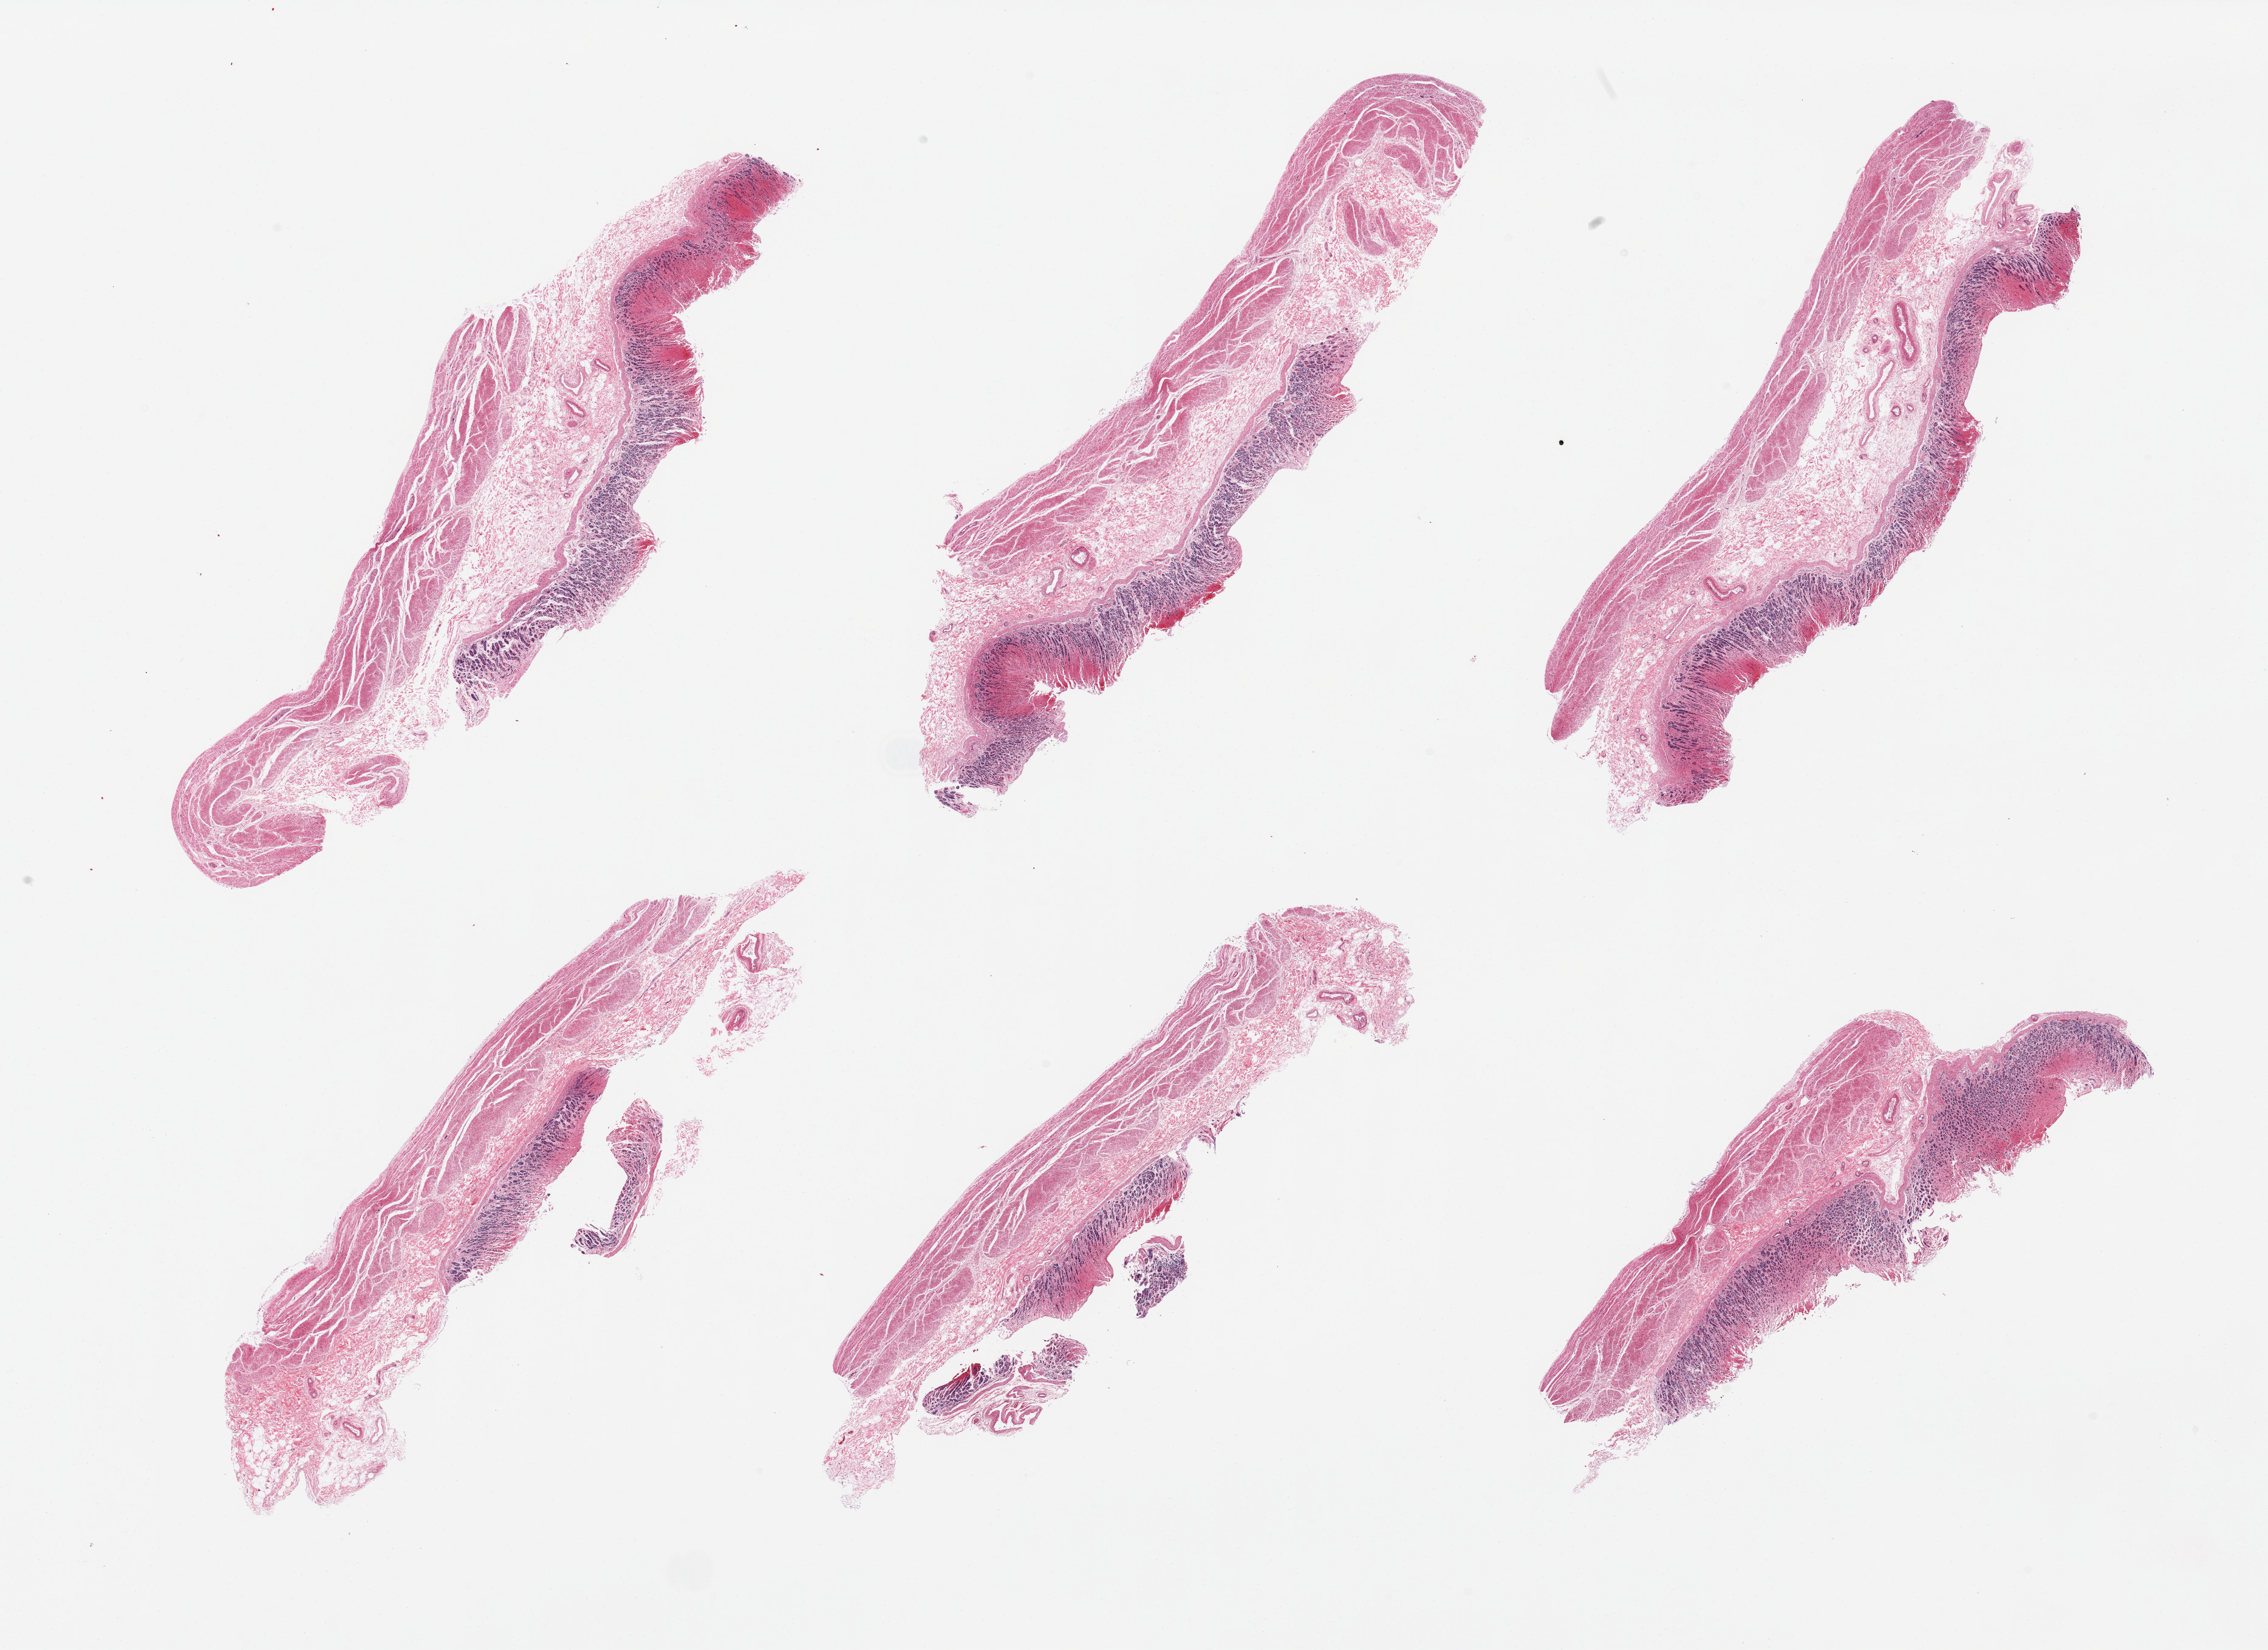
Digitized hematoxylin and eosin (H&E)-stained section, brightfield — low-resolution overview of the scanned area, about 29.5 x 21.5 mm (acquisition: 20x scan); PAXgene-fixed paraffin-embedded (PFPE) section; target tissue: stomach; tissue donor sample. Male donor.
Reviewer comment on this tissue sample: 6 pieces, mucosa ~1mm but modreately-severelay autolyzed, hemorrhagic.